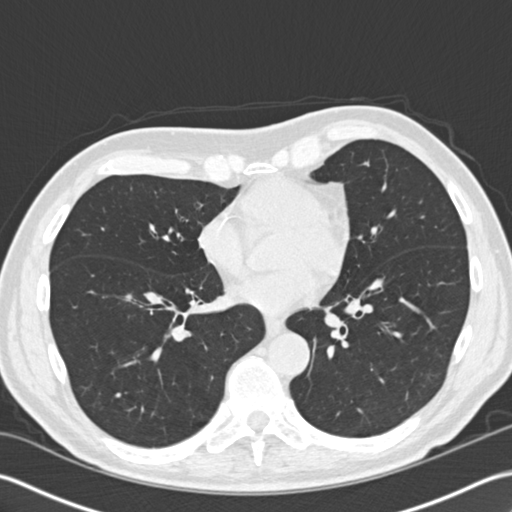
Axial slice from a low-dose chest CT screening exam. First (baseline) screen. Lung window (W 1500 / L -600 HU). 2 mm slice thickness. 120 kVp. Slice 98 of 168 in the series. 512 × 512 image matrix. Male participant, aged 73 years at enrolment.
Lesion marked by an expert reader, box from (x=106, y=277) to (x=150, y=321) px. Screening reader's record for this exam: no non-calcified nodule ≥4 mm recorded. Official screen result: negative screen, significant abnormalities not suspicious for lung cancer. Later outcome: lung cancer diagnosed 430 days after this screen (after the second annual screen) — non-small cell carcinoma, right lower lobe, stage IA (AJCC 6th edition), 30 mm at pathology.